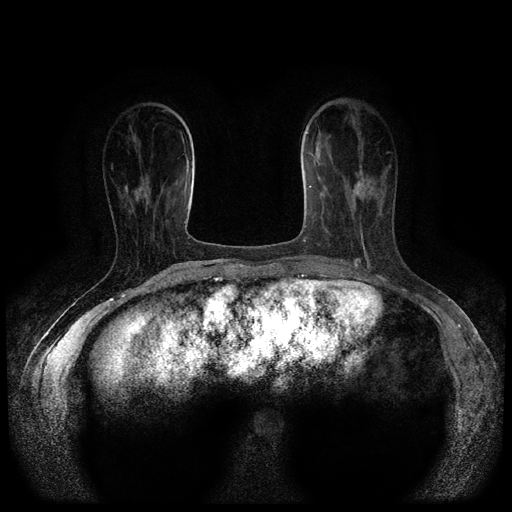
Breast MRI (dynamic contrast-enhanced, multi-phase), one axial slice; slice 30 of 116 in the series (ordered by position); dynamic contrast-enhanced series, time point 2 of 5 at this slice position (early post-contrast); 1.5 T; TE 2.6 ms, TR 5.4 ms; 2 mm slice thickness; 512 × 512 image matrix, field of view 340 × 340 mm. Patient: female, 47 years.
Annotated regions visible in this slice (semi-automatic segmentation, software-assisted and operator-edited):
- breast lesion (labelled 'tumour' in the annotation; benign lesions carry a separate 'benign' label): box from (x=351, y=176) to (x=365, y=209) px